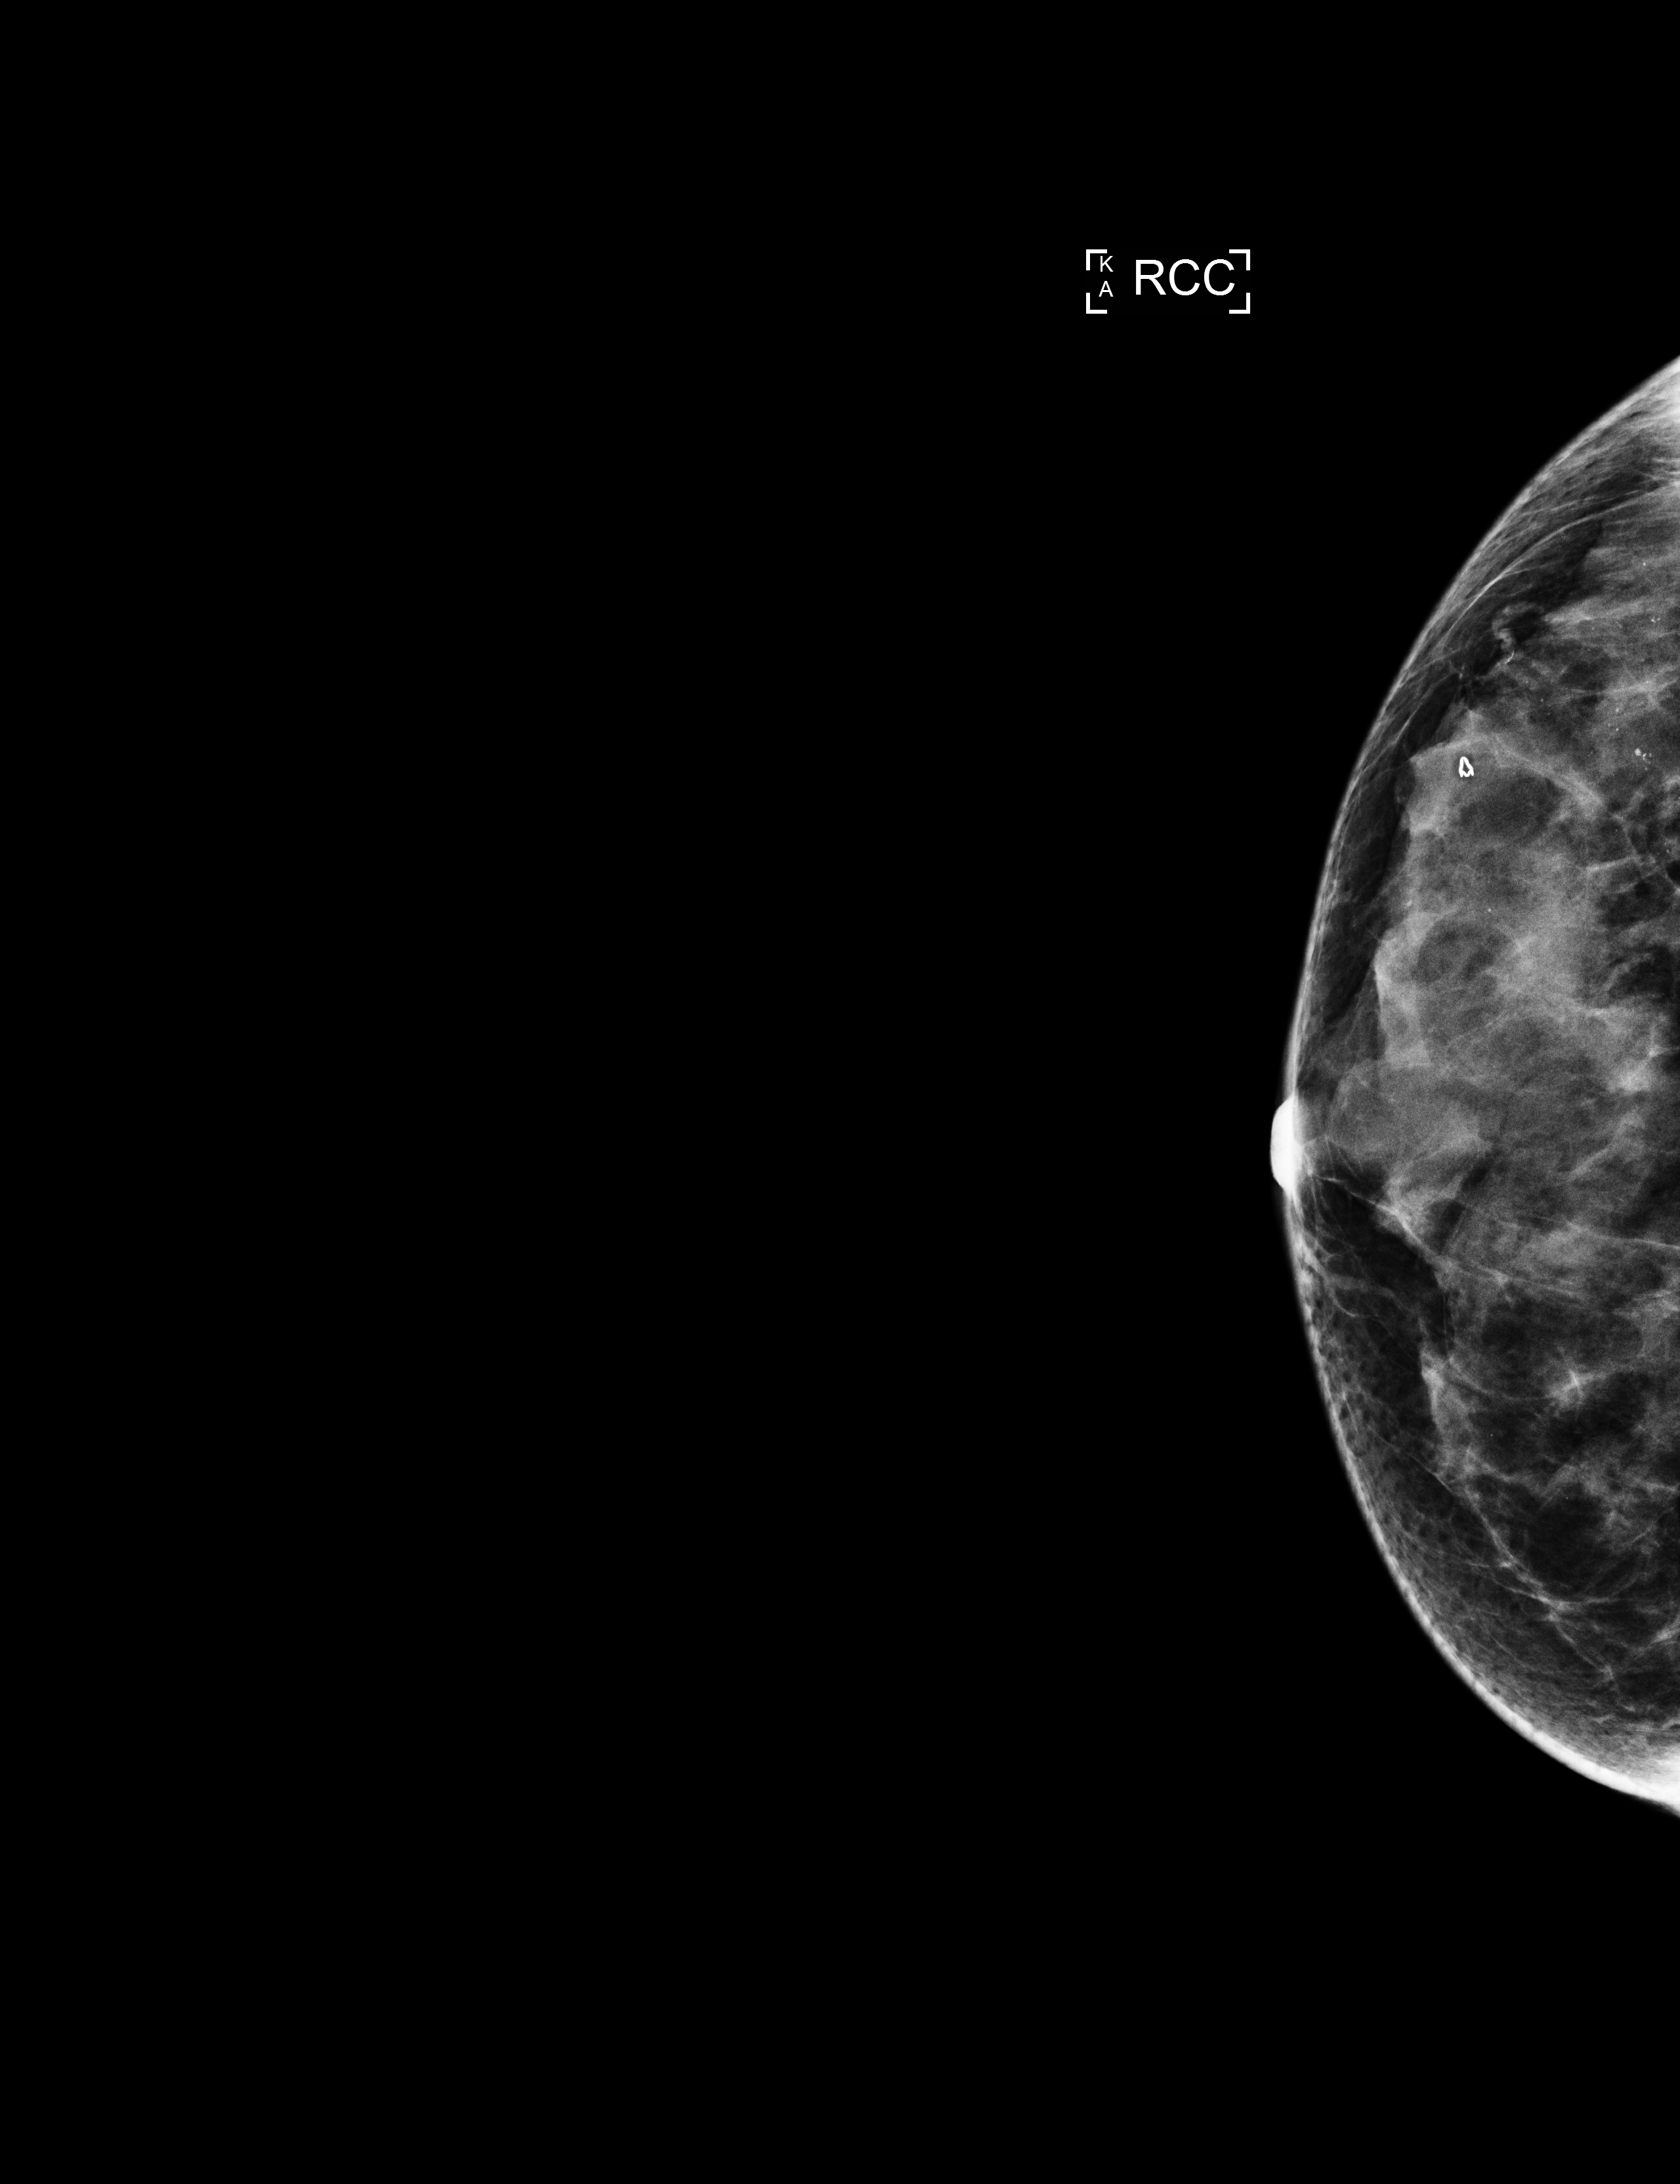
Screening examination; compressed breast thickness 36 mm. Female patient, age 59 years.
Image type: full-field digital mammogram. Breast: right. Projection: craniocaudal (CC) view.